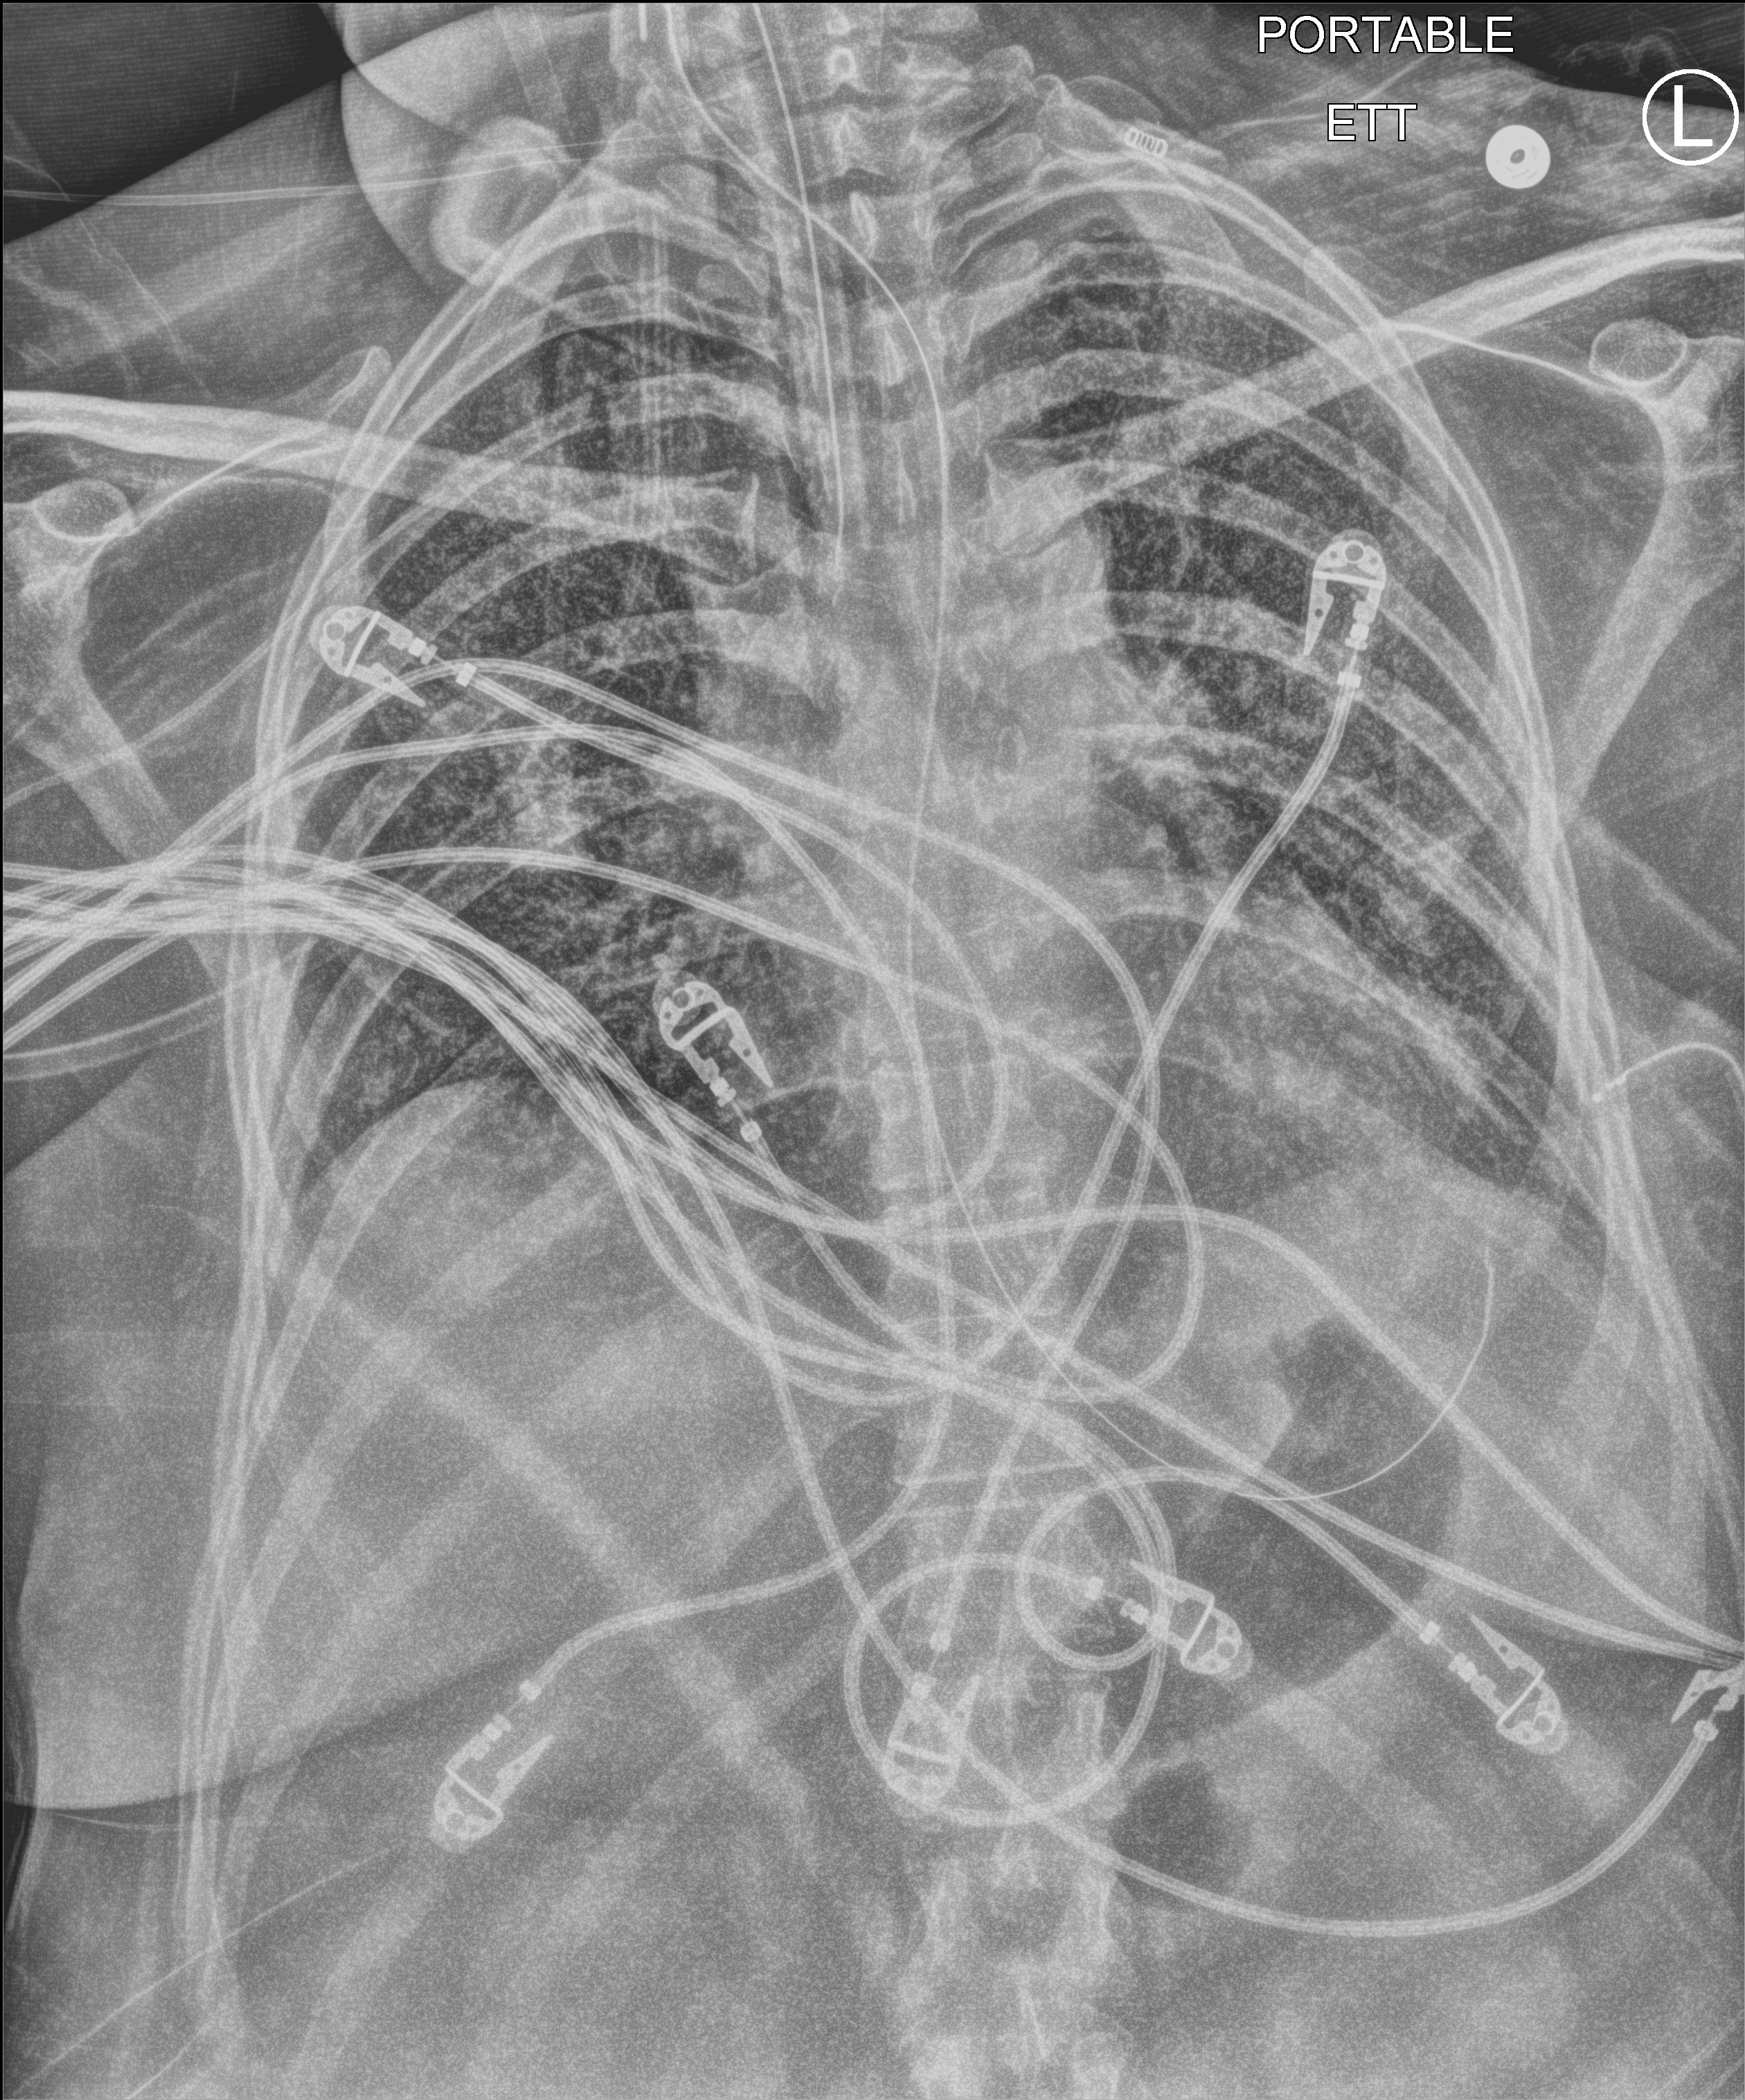
Portable chest radiograph. Female patient hospitalised with COVID-19, age 18–59 years.
Hospital-stay facts (about this admission, not read from this image; timing relative to this image not recorded): length of hospital stay: 73 days; admitted to intensive care during this hospital stay: yes; mechanically ventilated during this hospital stay: yes.